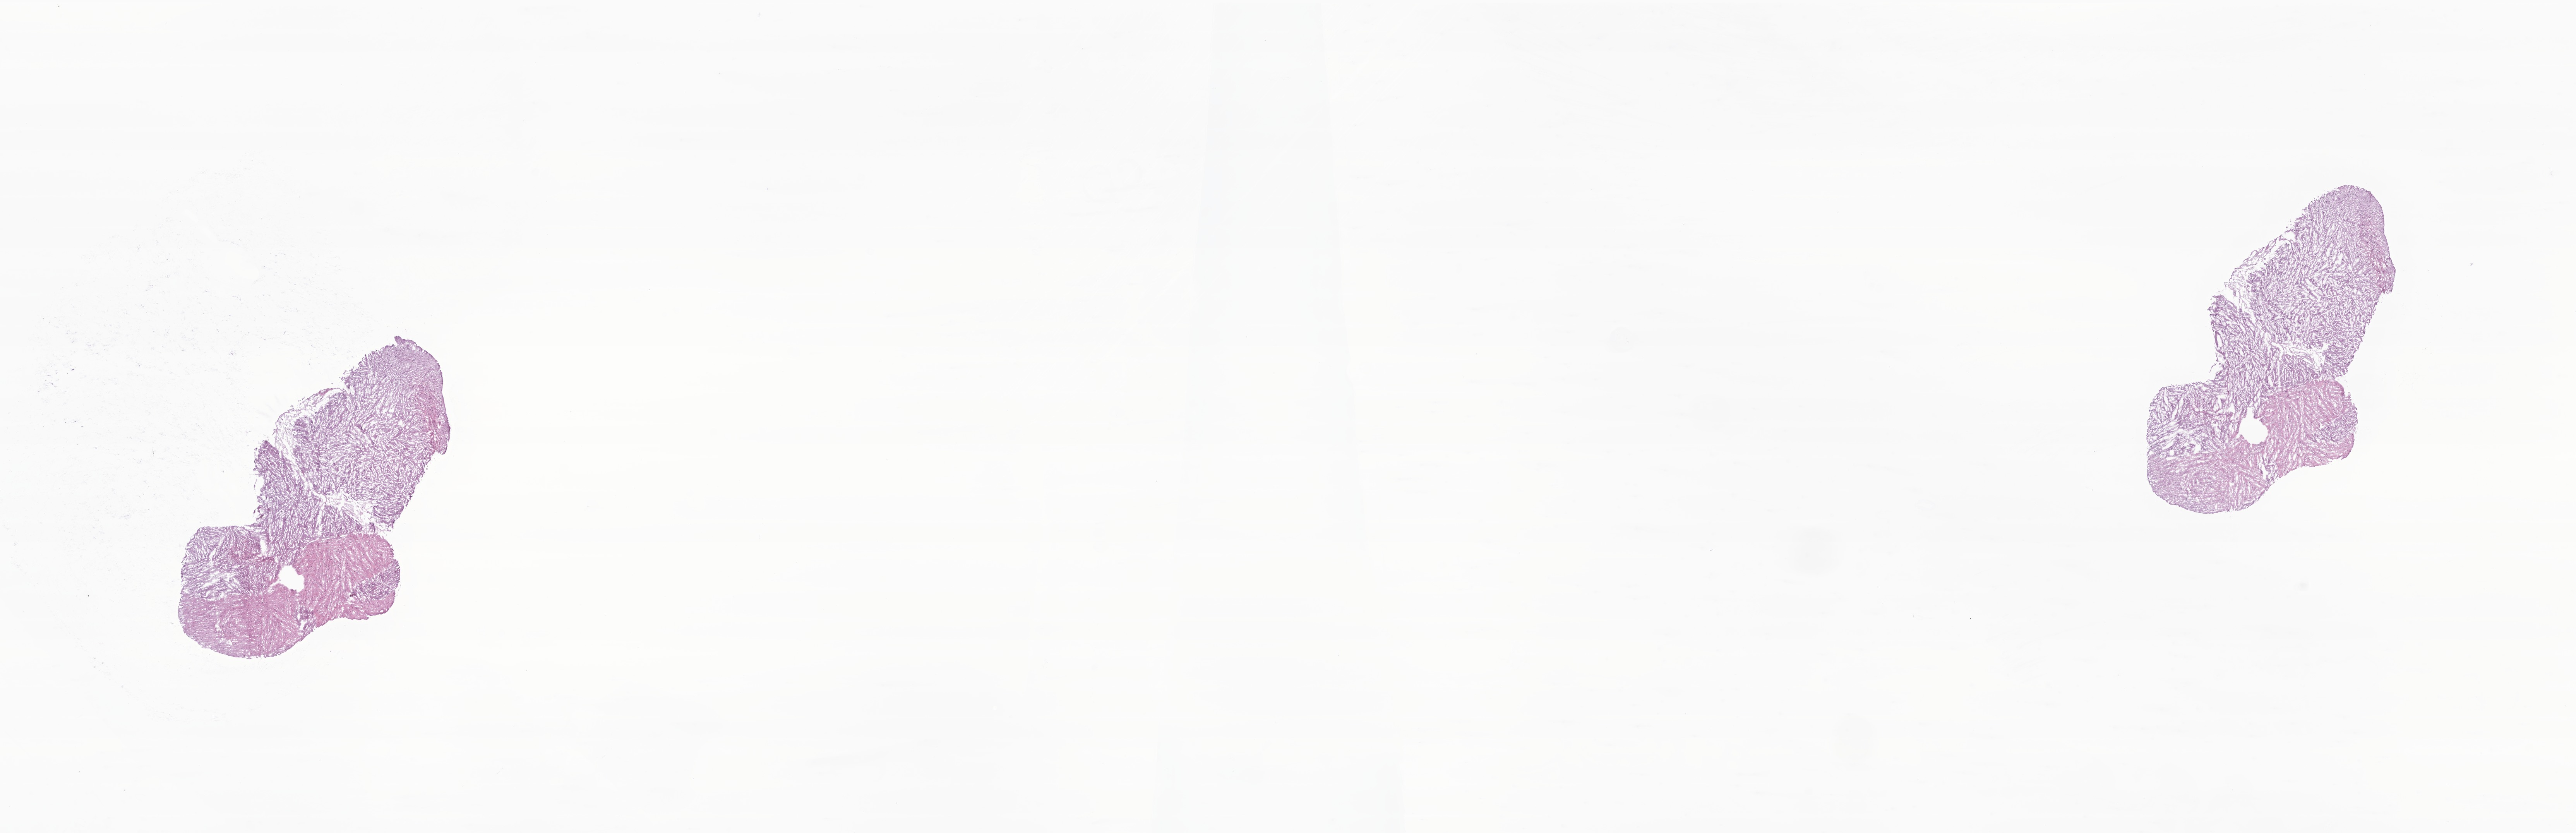
Whole-slide image, hematoxylin and eosin (H&E) stain of tumor tissue from the cerebrum, shown as a low-resolution overview of the whole scanned area (about 28.1 x 9.1 mm), frozen section (OCT-embedded). Male patient, age 107 months (8 years 11 months).
* diagnosis (ICD-O-3 morphology term): Glioma, malignant